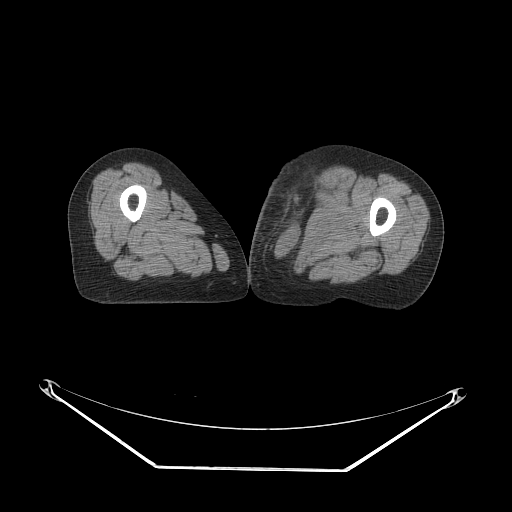
CT of an extremity soft-tissue mass (from a PET/CT study), one axial slice. Slice 47 of 91 in the series (ordered by position). 140 kVp. Soft-tissue window (W 400 / L 40 HU). 3.75 mm slice thickness. 512 × 512 image matrix. Female patient. From the clinical record (not read from this slice): histological type: pleomorphic leiomyosarcoma; grade: high; site of the primary tumour: left thigh.
Outlined on this slice (expert contour drawn on MRI and transferred to this co-registered scan by the dataset authors):
- gross tumour volume including surrounding oedema: bounding box [x1, y1, x2, y2] px = [263, 167, 334, 238]